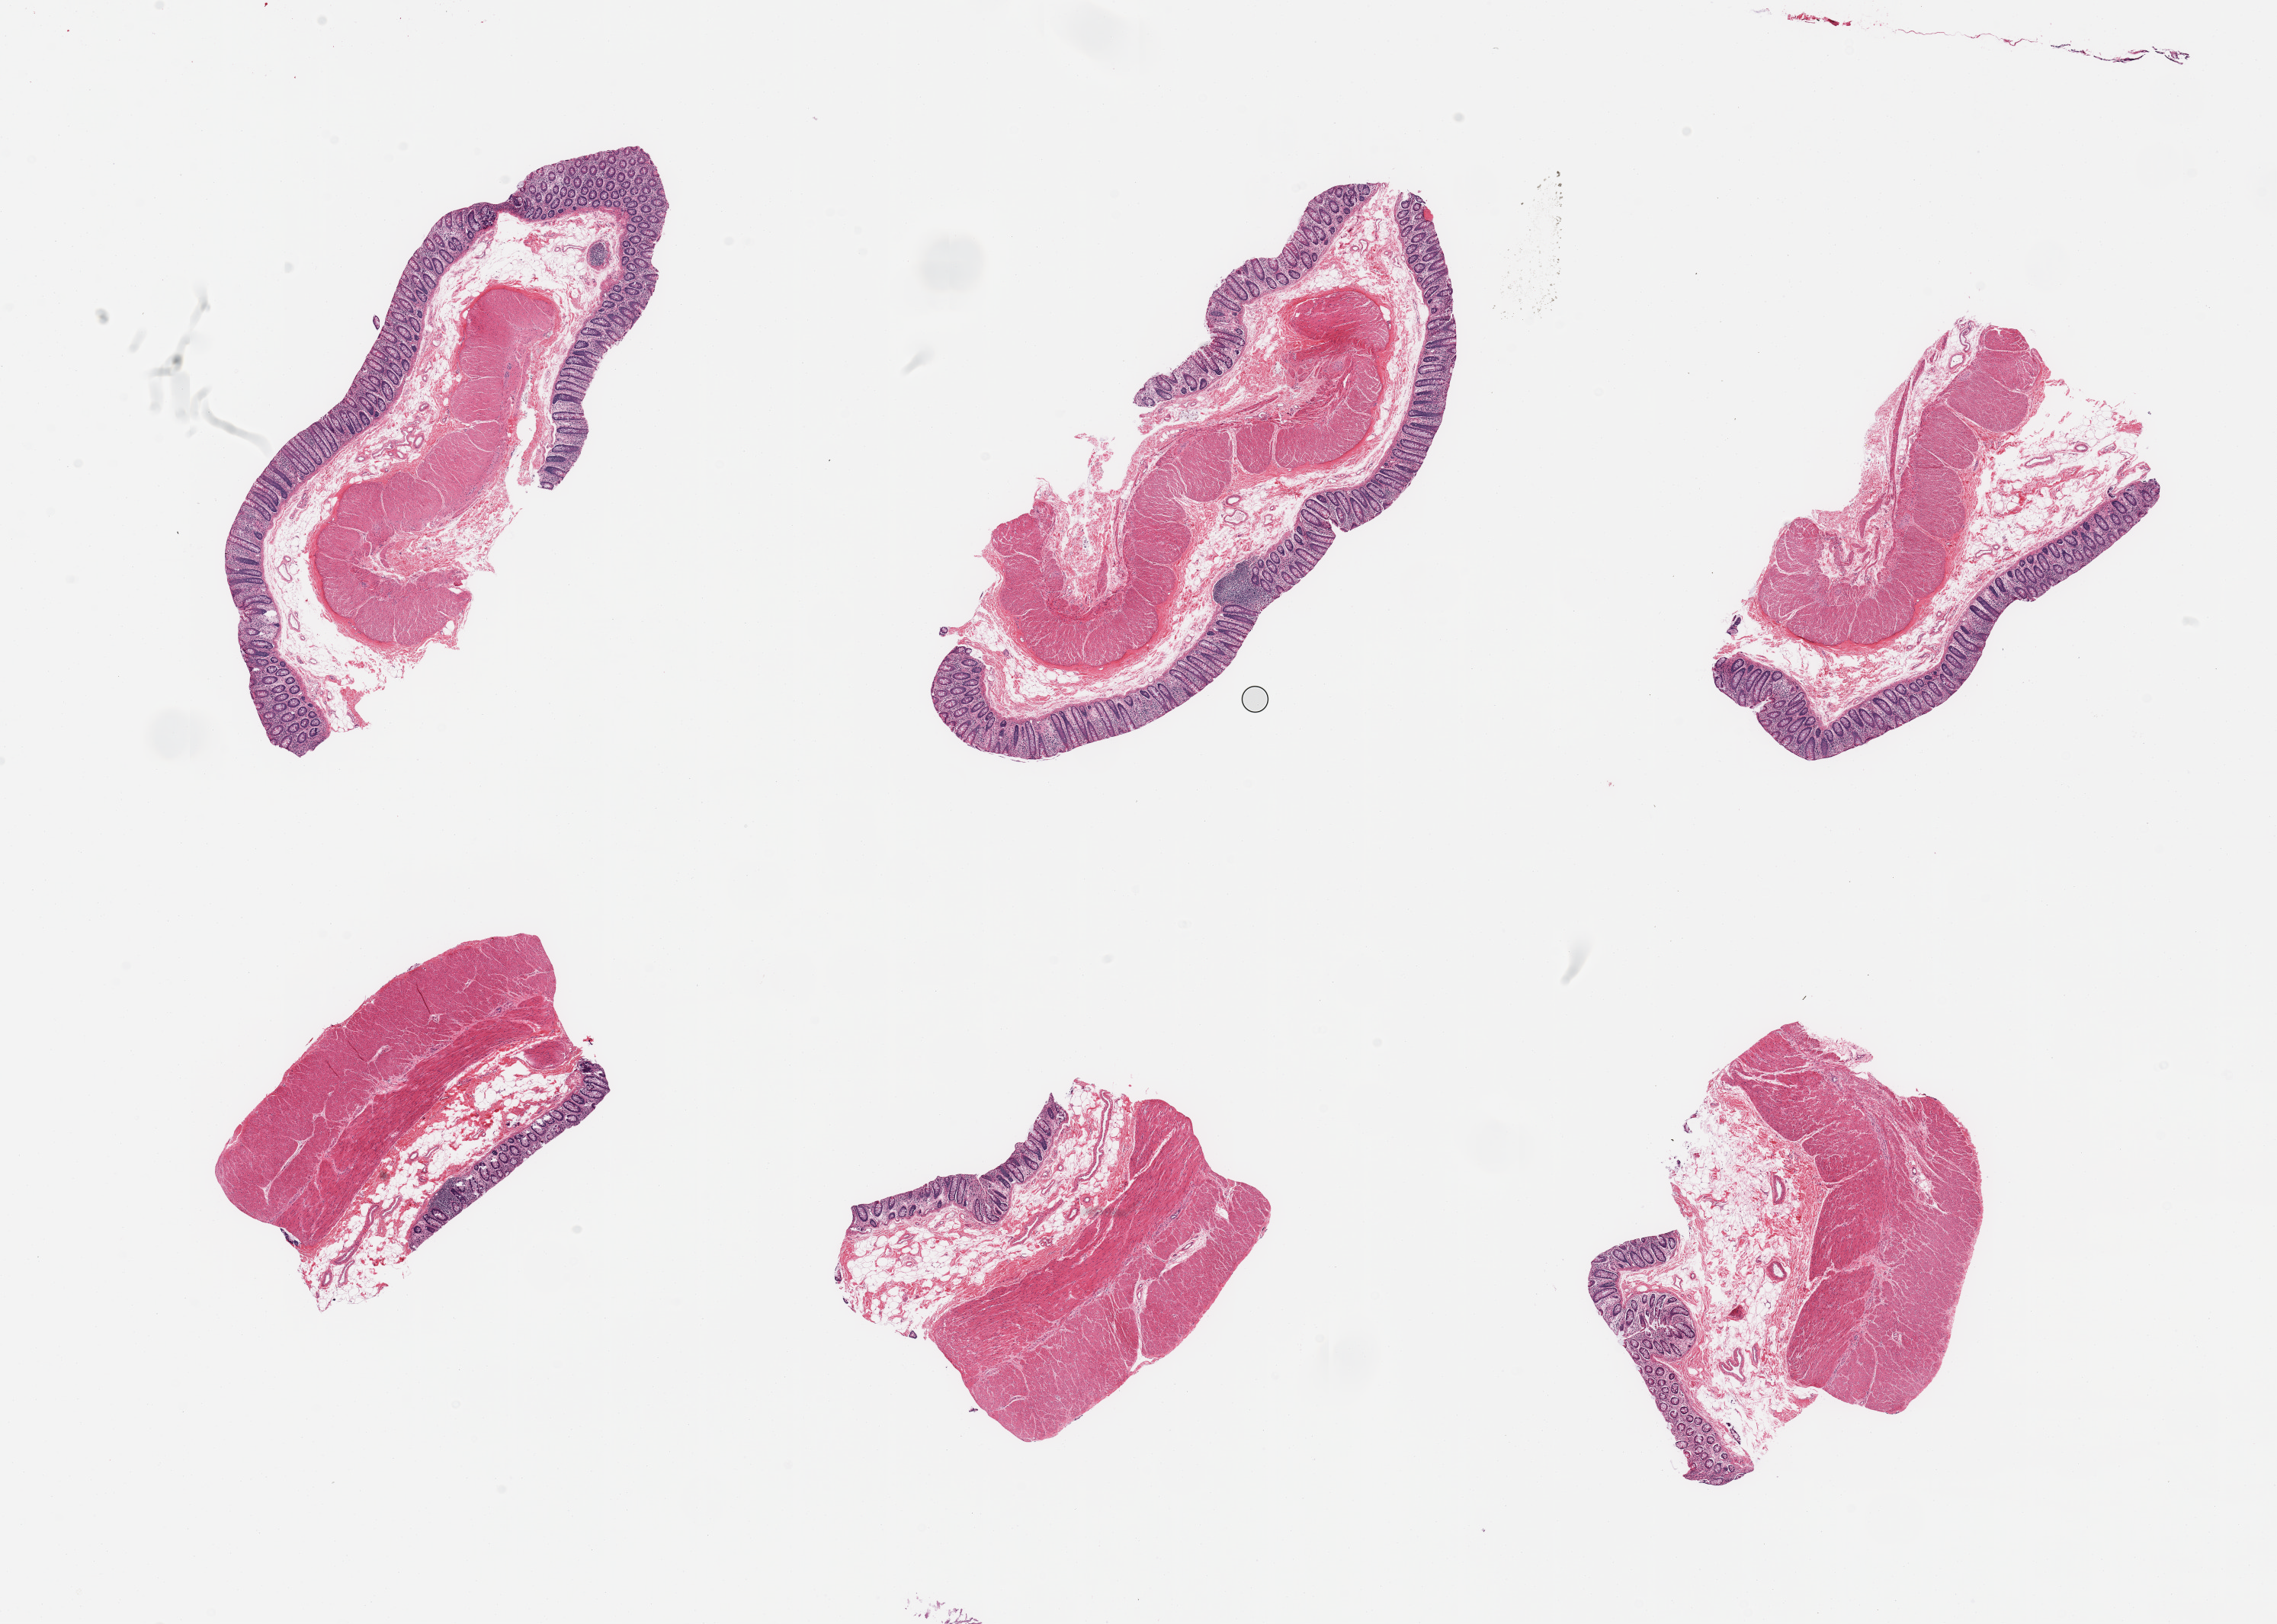
Hematoxylin and eosin (H&E) whole-slide image — a low-resolution overview of the entire scanned area, about 23.6 x 16.9 mm, PAXgene-fixed paraffin-embedded (PFPE) section, sampled site (target tissue): transverse colon, donor tissue sample. Male donor.
Pathologist's review note for this sample: 6 pieces; full thickness sections.